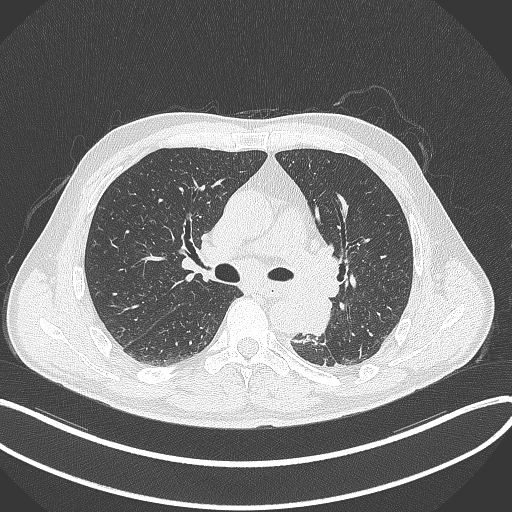
Chest CT, one axial slice; slice 208 of 329 in the series (ordered by position); 120 kVp; lung window (W 1500 / L -600 HU); 1 mm slice thickness; 512 × 512 image matrix, field of view 400 × 400 mm. Male patient, age 59 years. From the clinical record (not read from this slice): clinical TNM (as recorded): T2a N2 M0.
Annotated regions visible in this slice (bounding box drawn by a radiologist):
- lung tumour (recorded histology: squamous cell carcinoma): bounding box <297,289,333,336> (left, top, right, bottom; pixels)